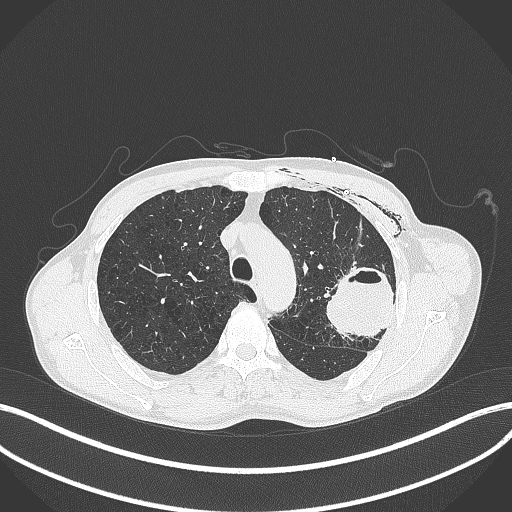
Chest CT, one axial slice; position 302 of 457 along the scan axis; lung window (W 1500 / L -600 HU); 512 × 512 image matrix, field of view 400 × 400 mm. Male patient, age 58 years. From the clinical record (not read from this slice): clinical TNM (as recorded): T3 N0 M0.
Outlined on this slice (rectangle marked by the reading radiologist):
- lung tumour (recorded histology: adenocarcinoma): bounding box (x1, y1, x2, y2) in pixels: (321, 264, 396, 344)